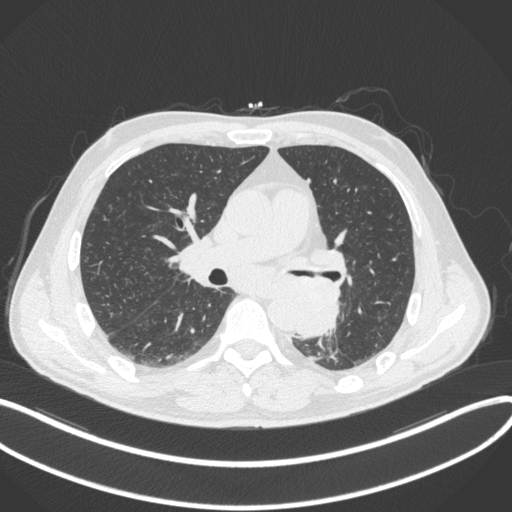
Chest CT, one axial slice; slice 191 of 328 in the series (ordered by position); reconstruction kernel B31f; 120 kVp; lung window (W 1500 / L -600 HU); 1 mm slice thickness; 512 × 512 image matrix. Male patient, age 59 years. Case-level facts recorded for this patient, not image findings: clinical TNM (as recorded): T2a N2 M0.
Structures marked on this image (bounding box drawn by a radiologist):
- lung tumour (recorded histology: squamous cell carcinoma): bounding box <288,285,346,340> (left, top, right, bottom; pixels)